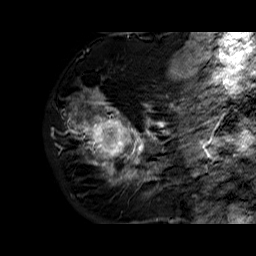
Breast MRI (dynamic contrast-enhanced), one sagittal slice. Position 20 of 60 along the scan axis. Dynamic contrast-enhanced series, time point 2 of 6 at this slice position (early post-contrast). 1.5 T. TE 6.3 ms, TR 32.4 ms. 4 mm slice thickness. 256 × 256 image matrix, field of view 200 × 200 mm. Female patient. Case-level facts recorded for this patient, not image findings: setting: breast cancer imaged before/during neoadjuvant chemotherapy; receptor status: HR-positive, HER2-negative.
Annotated regions visible in this slice (semi-automatic segmentation, software-assisted and operator-edited):
- analysis volume of interest (the breast-tissue region the enhancement analysis was run in; not a lesion): bounding box (x1, y1, x2, y2) in pixels: (69, 72, 177, 183)
- tumour enhancement mask (voxels above the 100 % enhancement threshold inside the analysis volume of interest): (73, 90, 175, 183)